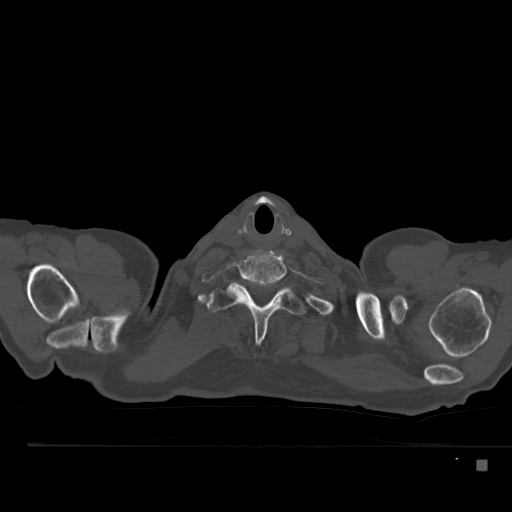
CT including the spine, one axial slice. Position 431 of 517 along the scan axis. Reconstruction kernel Br40s. 120 kVp. Bone window (W 1800 / L 400 HU). 1.5 mm slice thickness. 512 × 512 image matrix. Male patient, age 70 years. Case-level facts recorded for this patient, not image findings: primary cancer: renal; vertebrae with lytic lesions (as recorded): T4, T6, T10, T12, L3, L4, L5.
Structures marked on this image (semi-automatically segmented with operator editing):
- T1 vertebra: bounding box <204,283,309,343> (left, top, right, bottom; pixels)